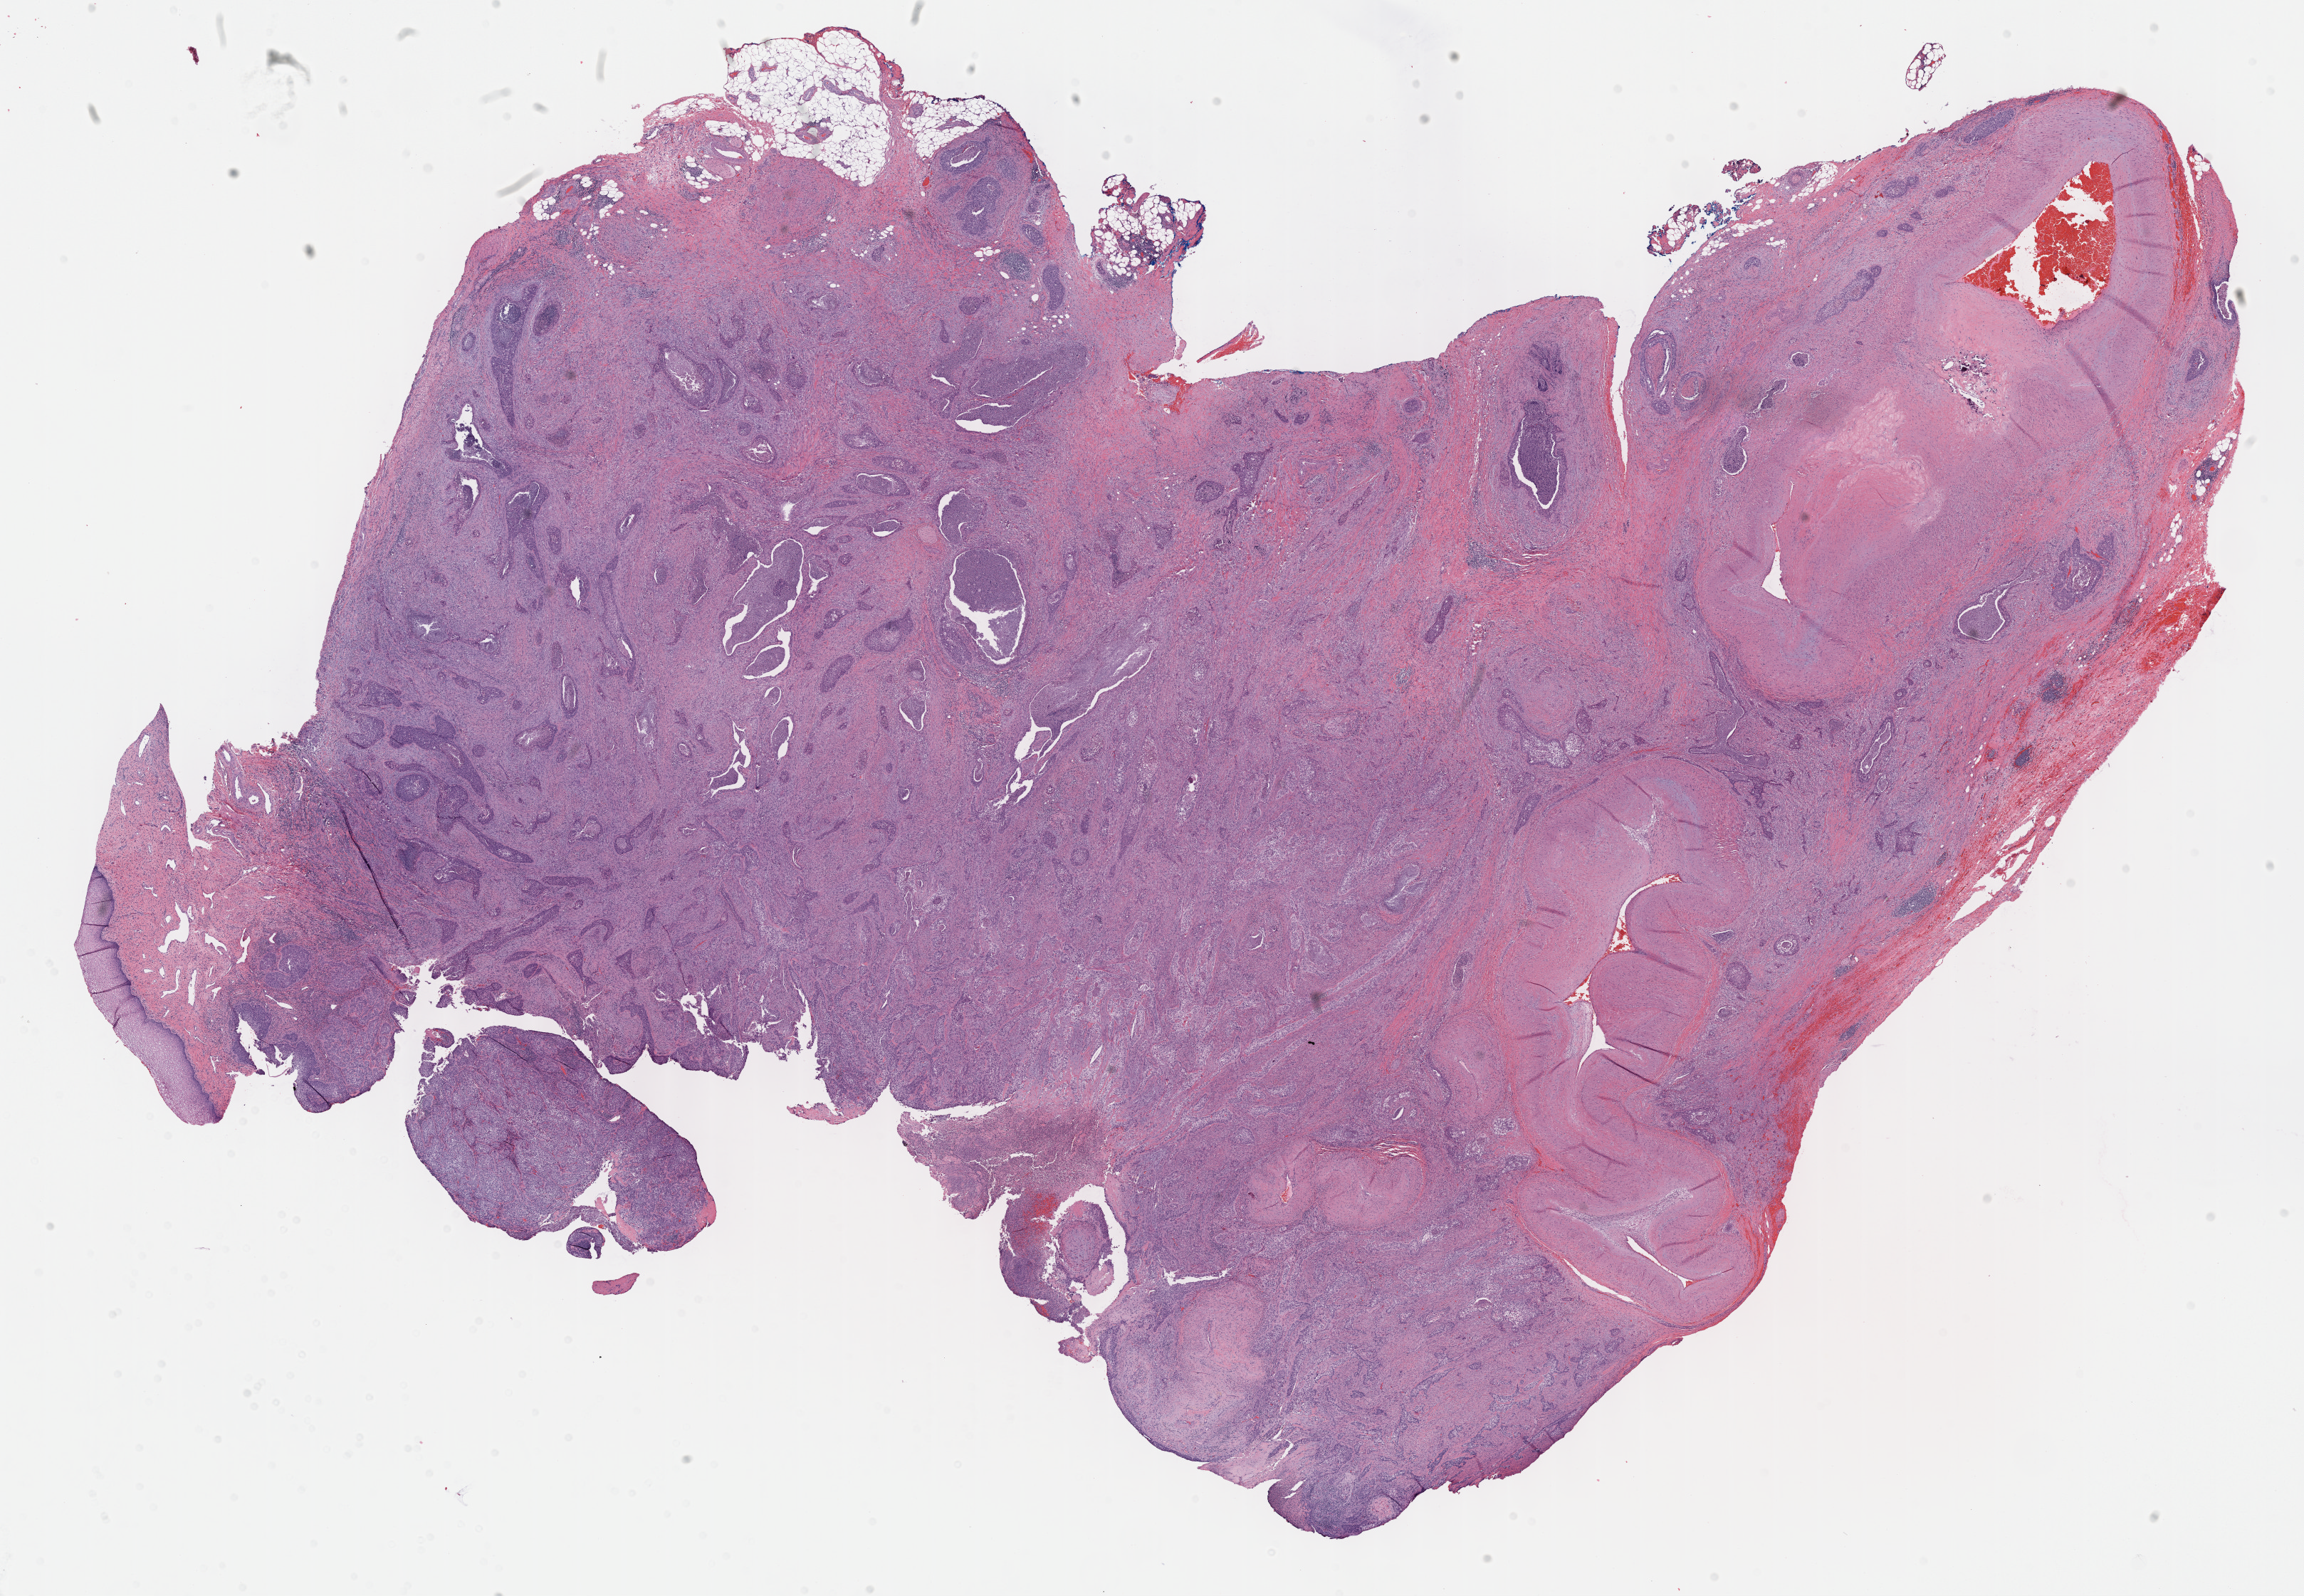
Whole-slide histology image, Hematoxylin and eosin (H&E) stained — whole scanned area (about 26.2 x 18.1 mm) shown as a low-resolution overview; formalin-fixed paraffin-embedded (FFPE) diagnostic section; primary tumour sample from the cervix. Female, age 49 years at initial diagnosis. Histologic grade: G3 (poorly differentiated).
FIGO stage: IIB. Pathologic diagnosis: Adenosquamous carcinoma.